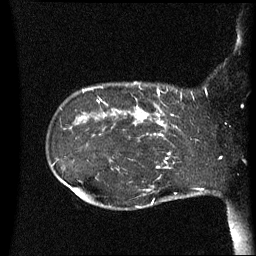
Breast MRI (dynamic contrast-enhanced), one sagittal slice. Dynamic contrast-enhanced series, image 2 of 3 at this slice position (ordered by acquisition). 1.5 T. TE 4.2 ms, TR 8.4 ms. 2.5 mm slice thickness. 256 × 256 image matrix, field of view 220 × 220 mm. Female patient, age 41 years. From the clinical record (not read from this slice): setting: breast cancer imaged before/during neoadjuvant chemotherapy; receptor status: HER2-positive.
Annotated regions visible in this slice (semi-automatic segmentation, software-assisted and operator-edited):
- analysis volume of interest (the breast-tissue region the enhancement analysis was run in; not a lesion): bounding box (x1, y1, x2, y2) in pixels: (122, 84, 195, 137)
- tumour enhancement mask (voxels above the 70 % enhancement threshold inside the analysis volume of interest): (126, 90, 166, 137)